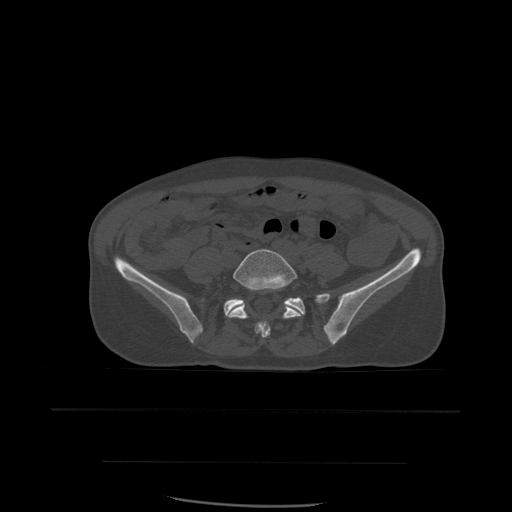
CT including the spine, one axial slice; position 141 of 574 along the scan axis; bone window (W 1800 / L 400 HU); 512 × 512 image matrix. Patient age 48 years. From the clinical record (not read from this slice): primary cancer: lung; vertebrae with lytic lesions (as recorded): T11.
Structures marked on this image (semi-automatically segmented with operator editing):
- L5 vertebra: bounding box (x1, y1, x2, y2) in pixels: (229, 249, 304, 339)